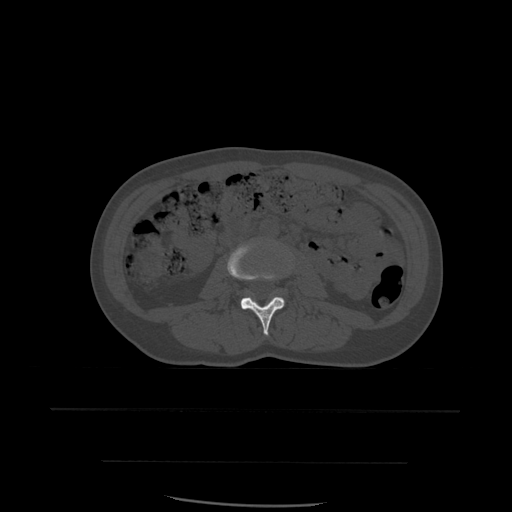
CT including the spine, one axial slice. Position 190 of 574 along the scan axis. Bone window (W 1800 / L 400 HU). 1.25 mm slice thickness. 512 × 512 image matrix, field of view 392 × 392 mm. Patient age 48 years. From the clinical record (not read from this slice): primary cancer: lung.
Annotated regions visible in this slice (semi-automatic segmentation, software-assisted and operator-edited):
- L3 vertebra: bounding box [x1, y1, x2, y2] px = [227, 243, 292, 337]